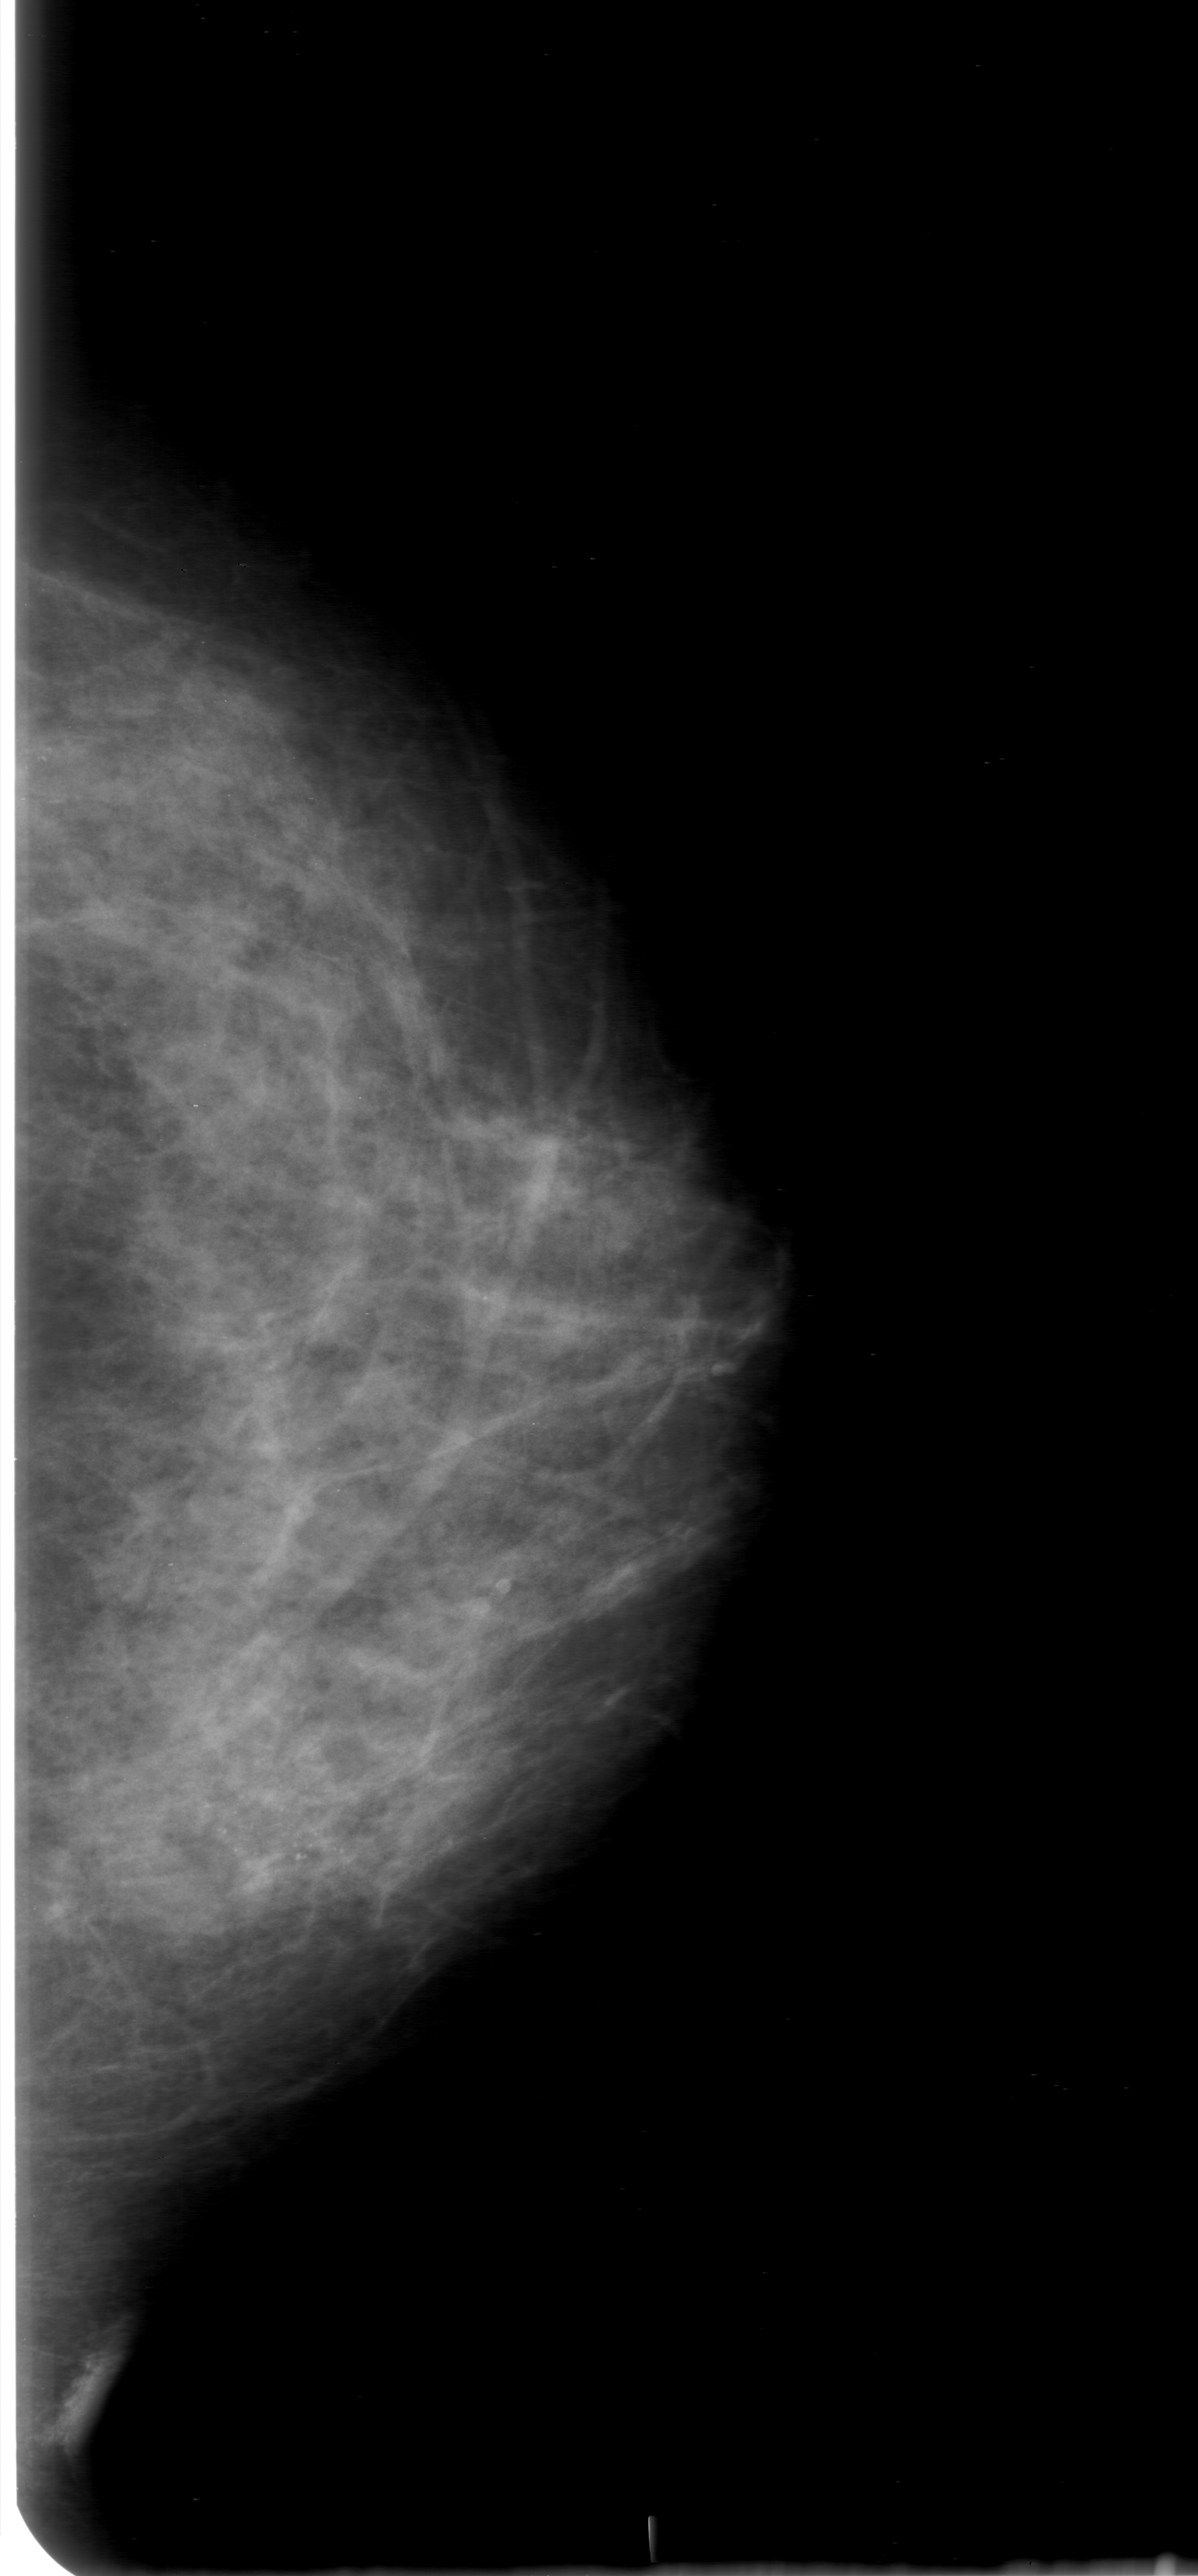
Digitized screen-film mammogram, left breast, craniocaudal (CC) view, breast composition: heterogeneously dense (BI-RADS density category 3 of 4).
Abnormality record for this image: calcifications, morphology pleomorphic, distribution clustered; BI-RADS assessment category 0 (incomplete: needs additional imaging); subtlety rating 4 on a 1 (subtle) to 5 (obvious) scale; pathology (as recorded): malignant.